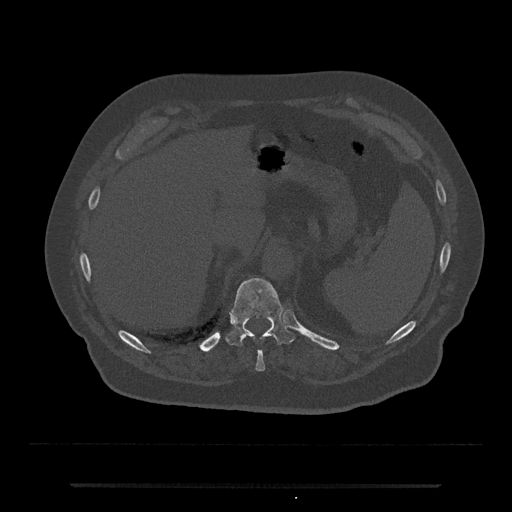
CT including the spine, one axial slice; slice 663 of 797 in the series (ordered by position); bone window (W 1800 / L 400 HU); 0.5 mm slice thickness; 512 × 512 image matrix, field of view 434 × 434 mm. Male patient, age 80 years. From the clinical record (not read from this slice): primary cancer: prostate; vertebrae with lytic lesions (as recorded): L1, T11.
Outlined on this slice (semi-automatic segmentation, software-assisted and operator-edited):
- T10 vertebra: box from (x=255, y=351) to (x=265, y=371) px
- T11 vertebra: (x=226, y=277)–(x=295, y=346)